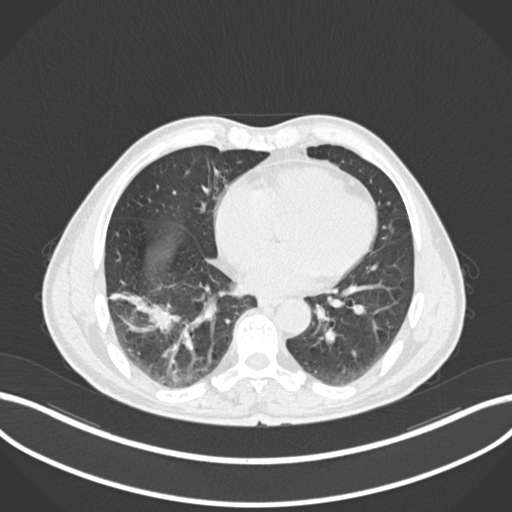
Chest CT, one axial slice. Slice 62 of 208 in the series (ordered by position). Reconstruction kernel B30f. Lung window (W 1500 / L -600 HU). 1 mm slice thickness. 512 × 512 image matrix, field of view 400 × 400 mm. Male patient, age 58 years. From the clinical record (not read from this slice): clinical TNM (as recorded): T3 N0 M0.
Annotated regions visible in this slice (bounding box drawn by a radiologist):
- lung tumour (recorded histology: squamous cell carcinoma): box from (x=114, y=289) to (x=181, y=339) px